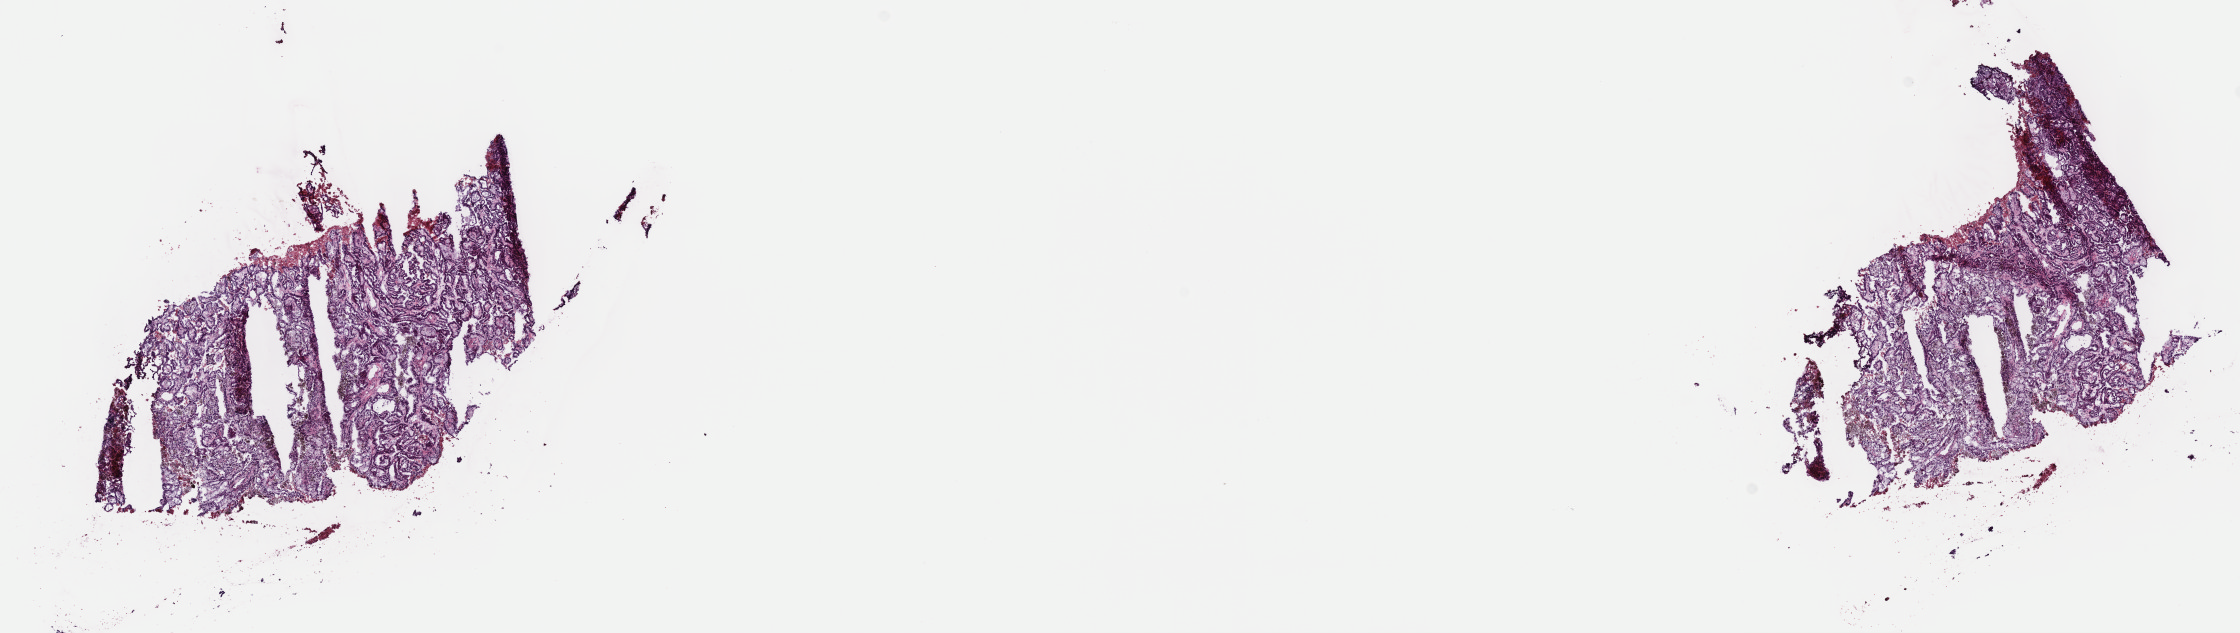
Digitized Hematoxylin and eosin (H&E) stained tissue section (whole slide) — whole scanned area (about 18.1 x 5.1 mm) shown as a low-resolution overview; frozen section from the top of the tissue portion; primary tumour sample from the kidney. Male patient; age at initial diagnosis 71 years.
Diagnosis: Papillary adenocarcinoma, NOS.